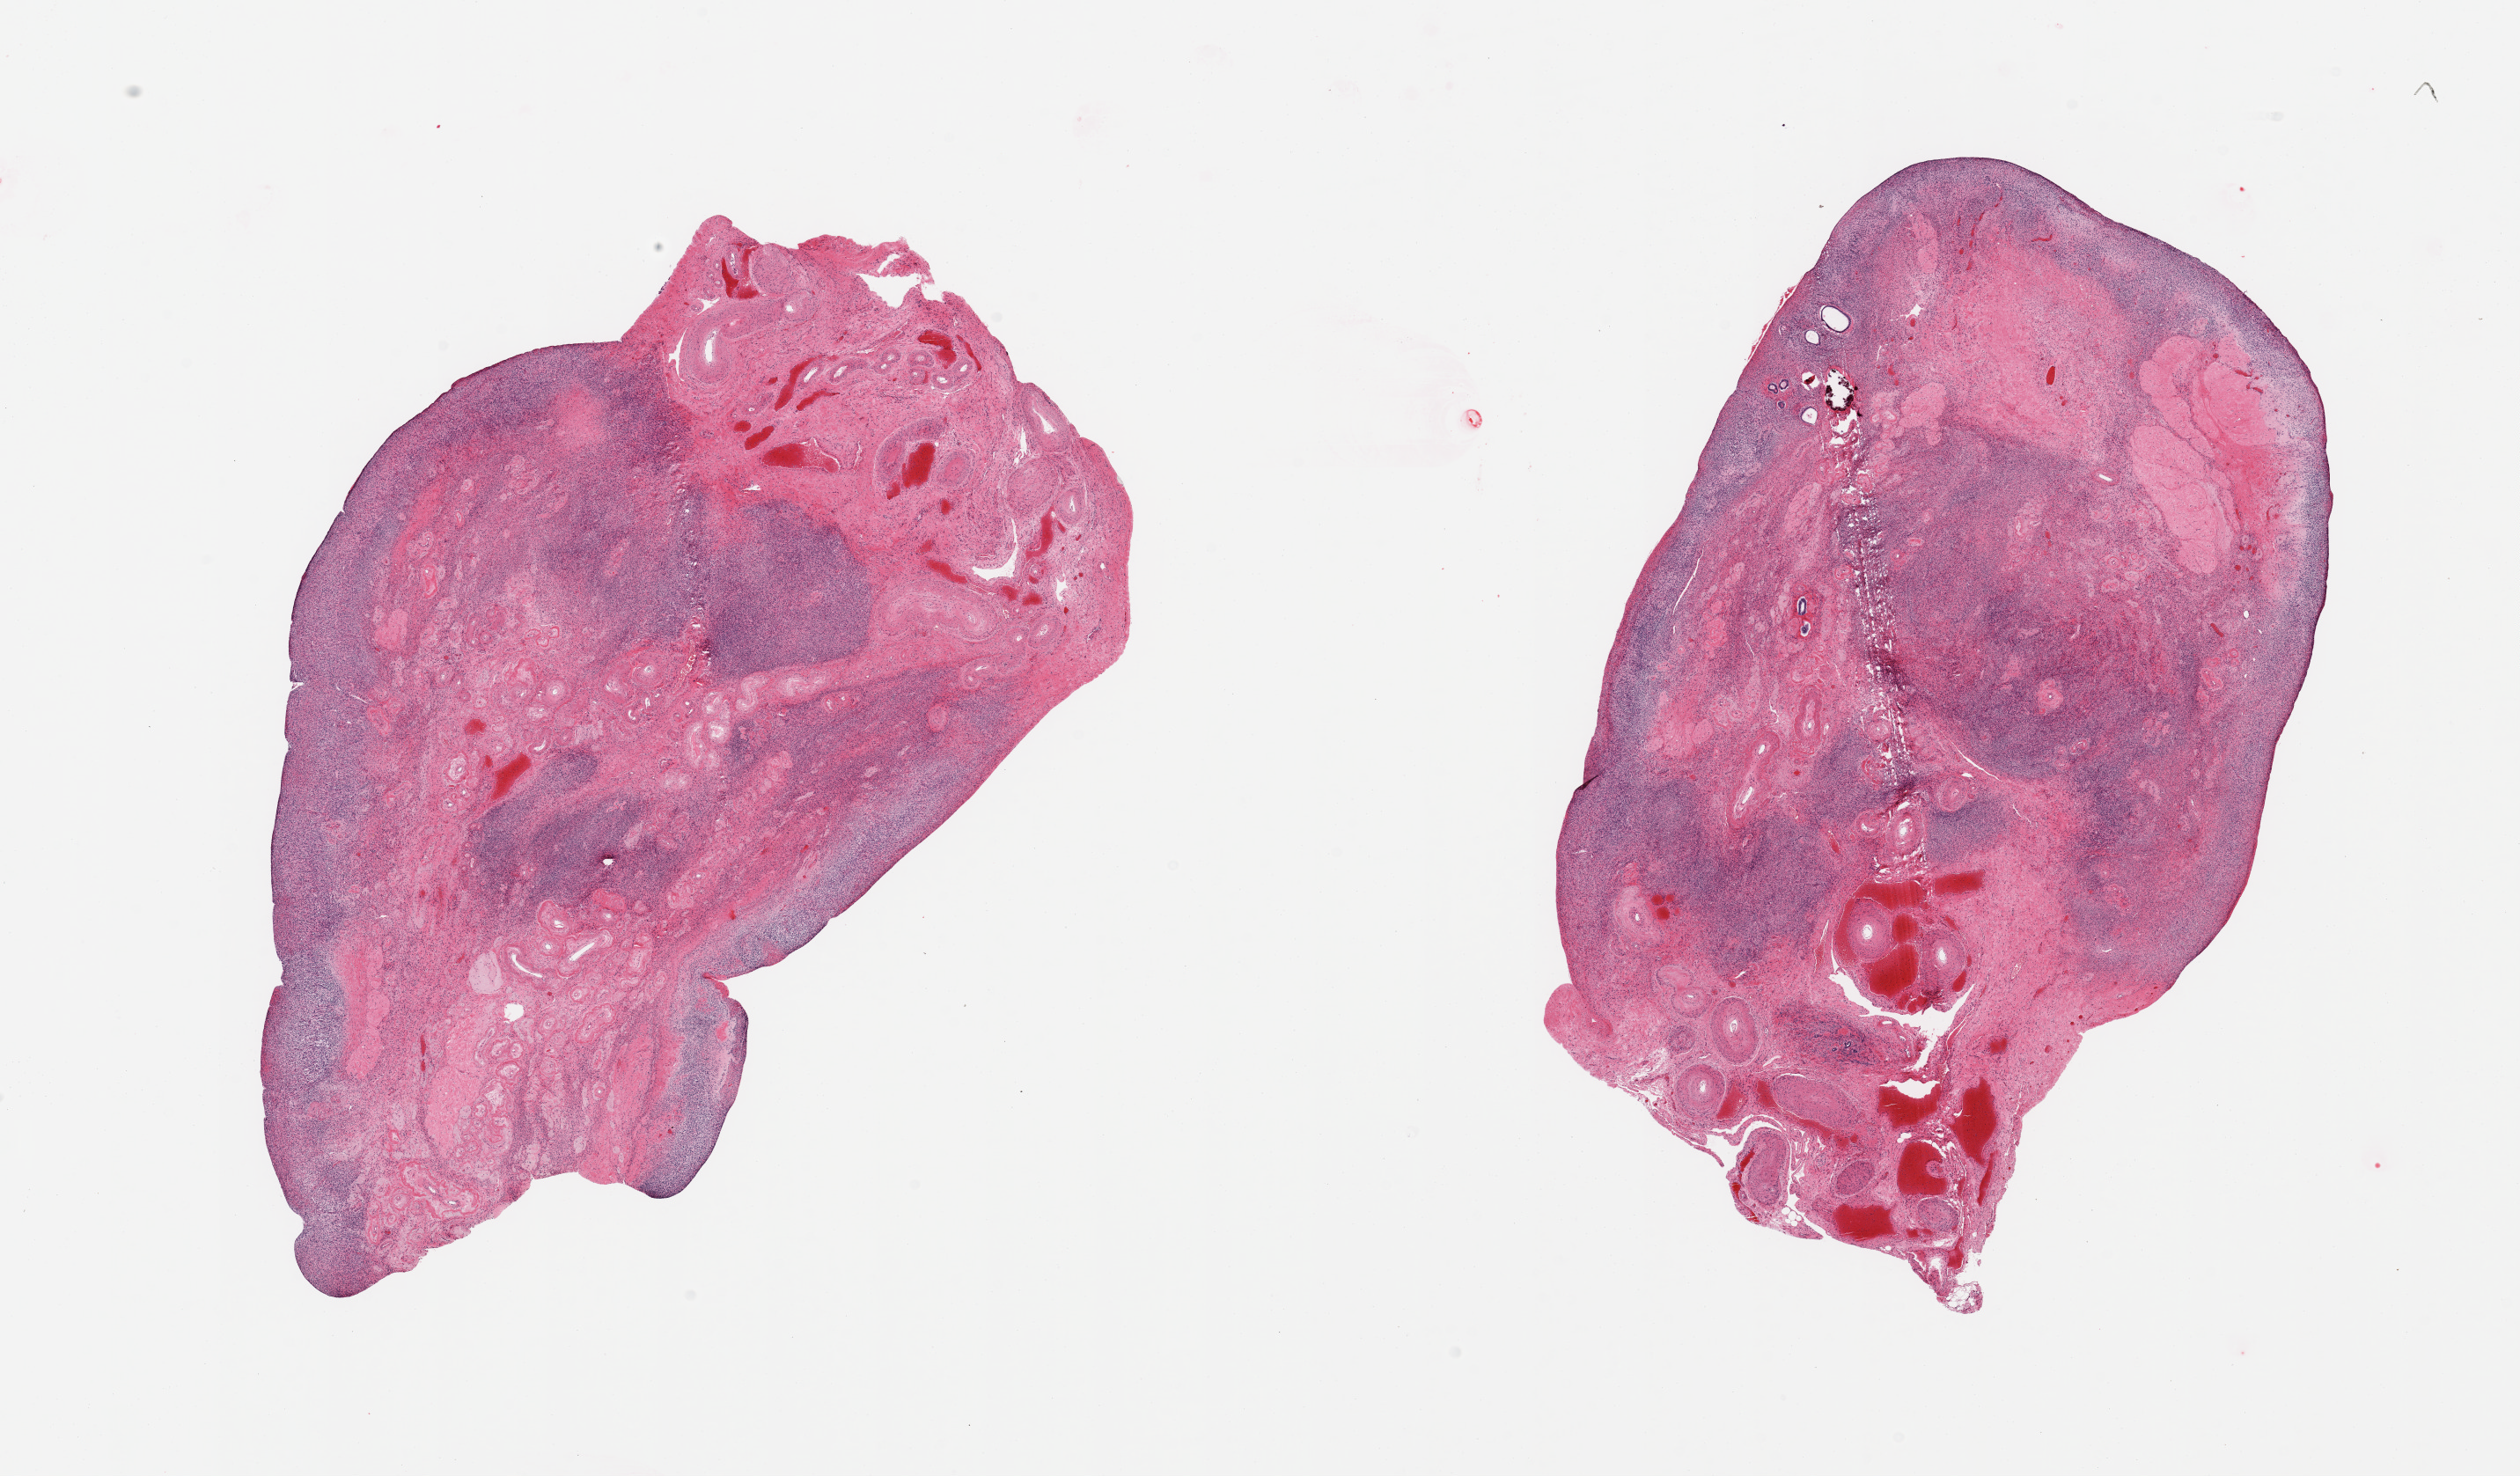
Whole-slide image, H&E stain, brightfield — a low-resolution overview of the entire scanned area, about 22.6 x 13.3 mm. PAXgene-fixed, paraffin-embedded tissue. Target tissue: ovary. Donor tissue sample. Donor: female.
Reviewer comment on this tissue sample: 2 pieces; few inclusion glands and focus of calcification.